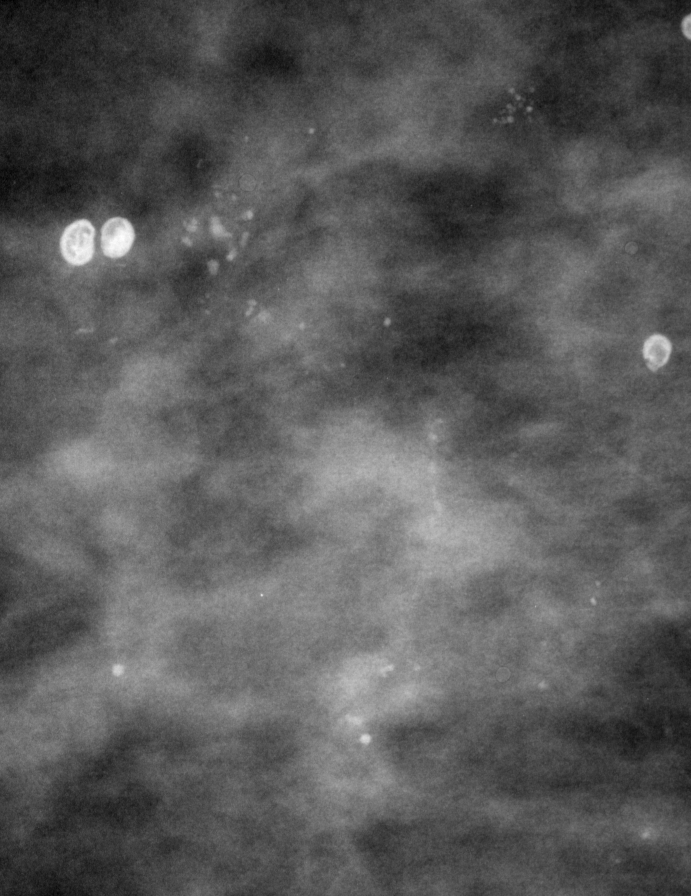
Region of interest cut from a scanned film mammogram (one marked finding), left breast, CC view.
- Calcifications, morphology pleomorphic, distribution segmental; BI-RADS assessment category 4; subtlety rating 3 on a 1 (subtle) to 5 (obvious) scale; pathology (as recorded): malignant.